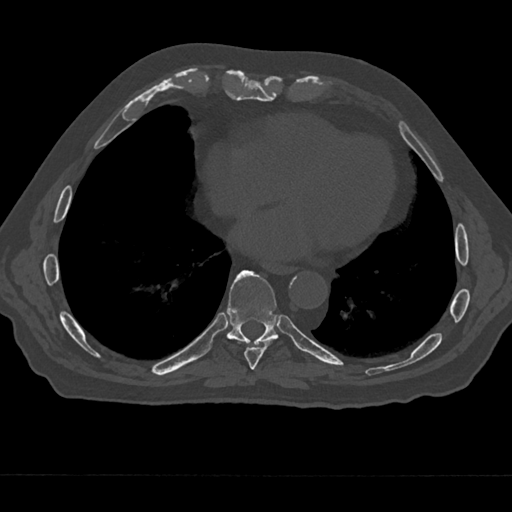
CT including the spine, one axial slice. Position 287 of 797 along the scan axis. 120 kVp. Bone window (W 1800 / L 400 HU). 512 × 512 image matrix, field of view 377 × 377 mm. Male patient, age 75 years. From the clinical record (not read from this slice): primary cancer: renal; vertebrae with lytic lesions (as recorded): T4.
Outlined on this slice (semi-automatically segmented with operator editing):
- T7 vertebra: bounding box <249,379,252,382> (left, top, right, bottom; pixels)
- T8 vertebra: <238,339,274,370>
- T9 vertebra: <225,270,288,352>